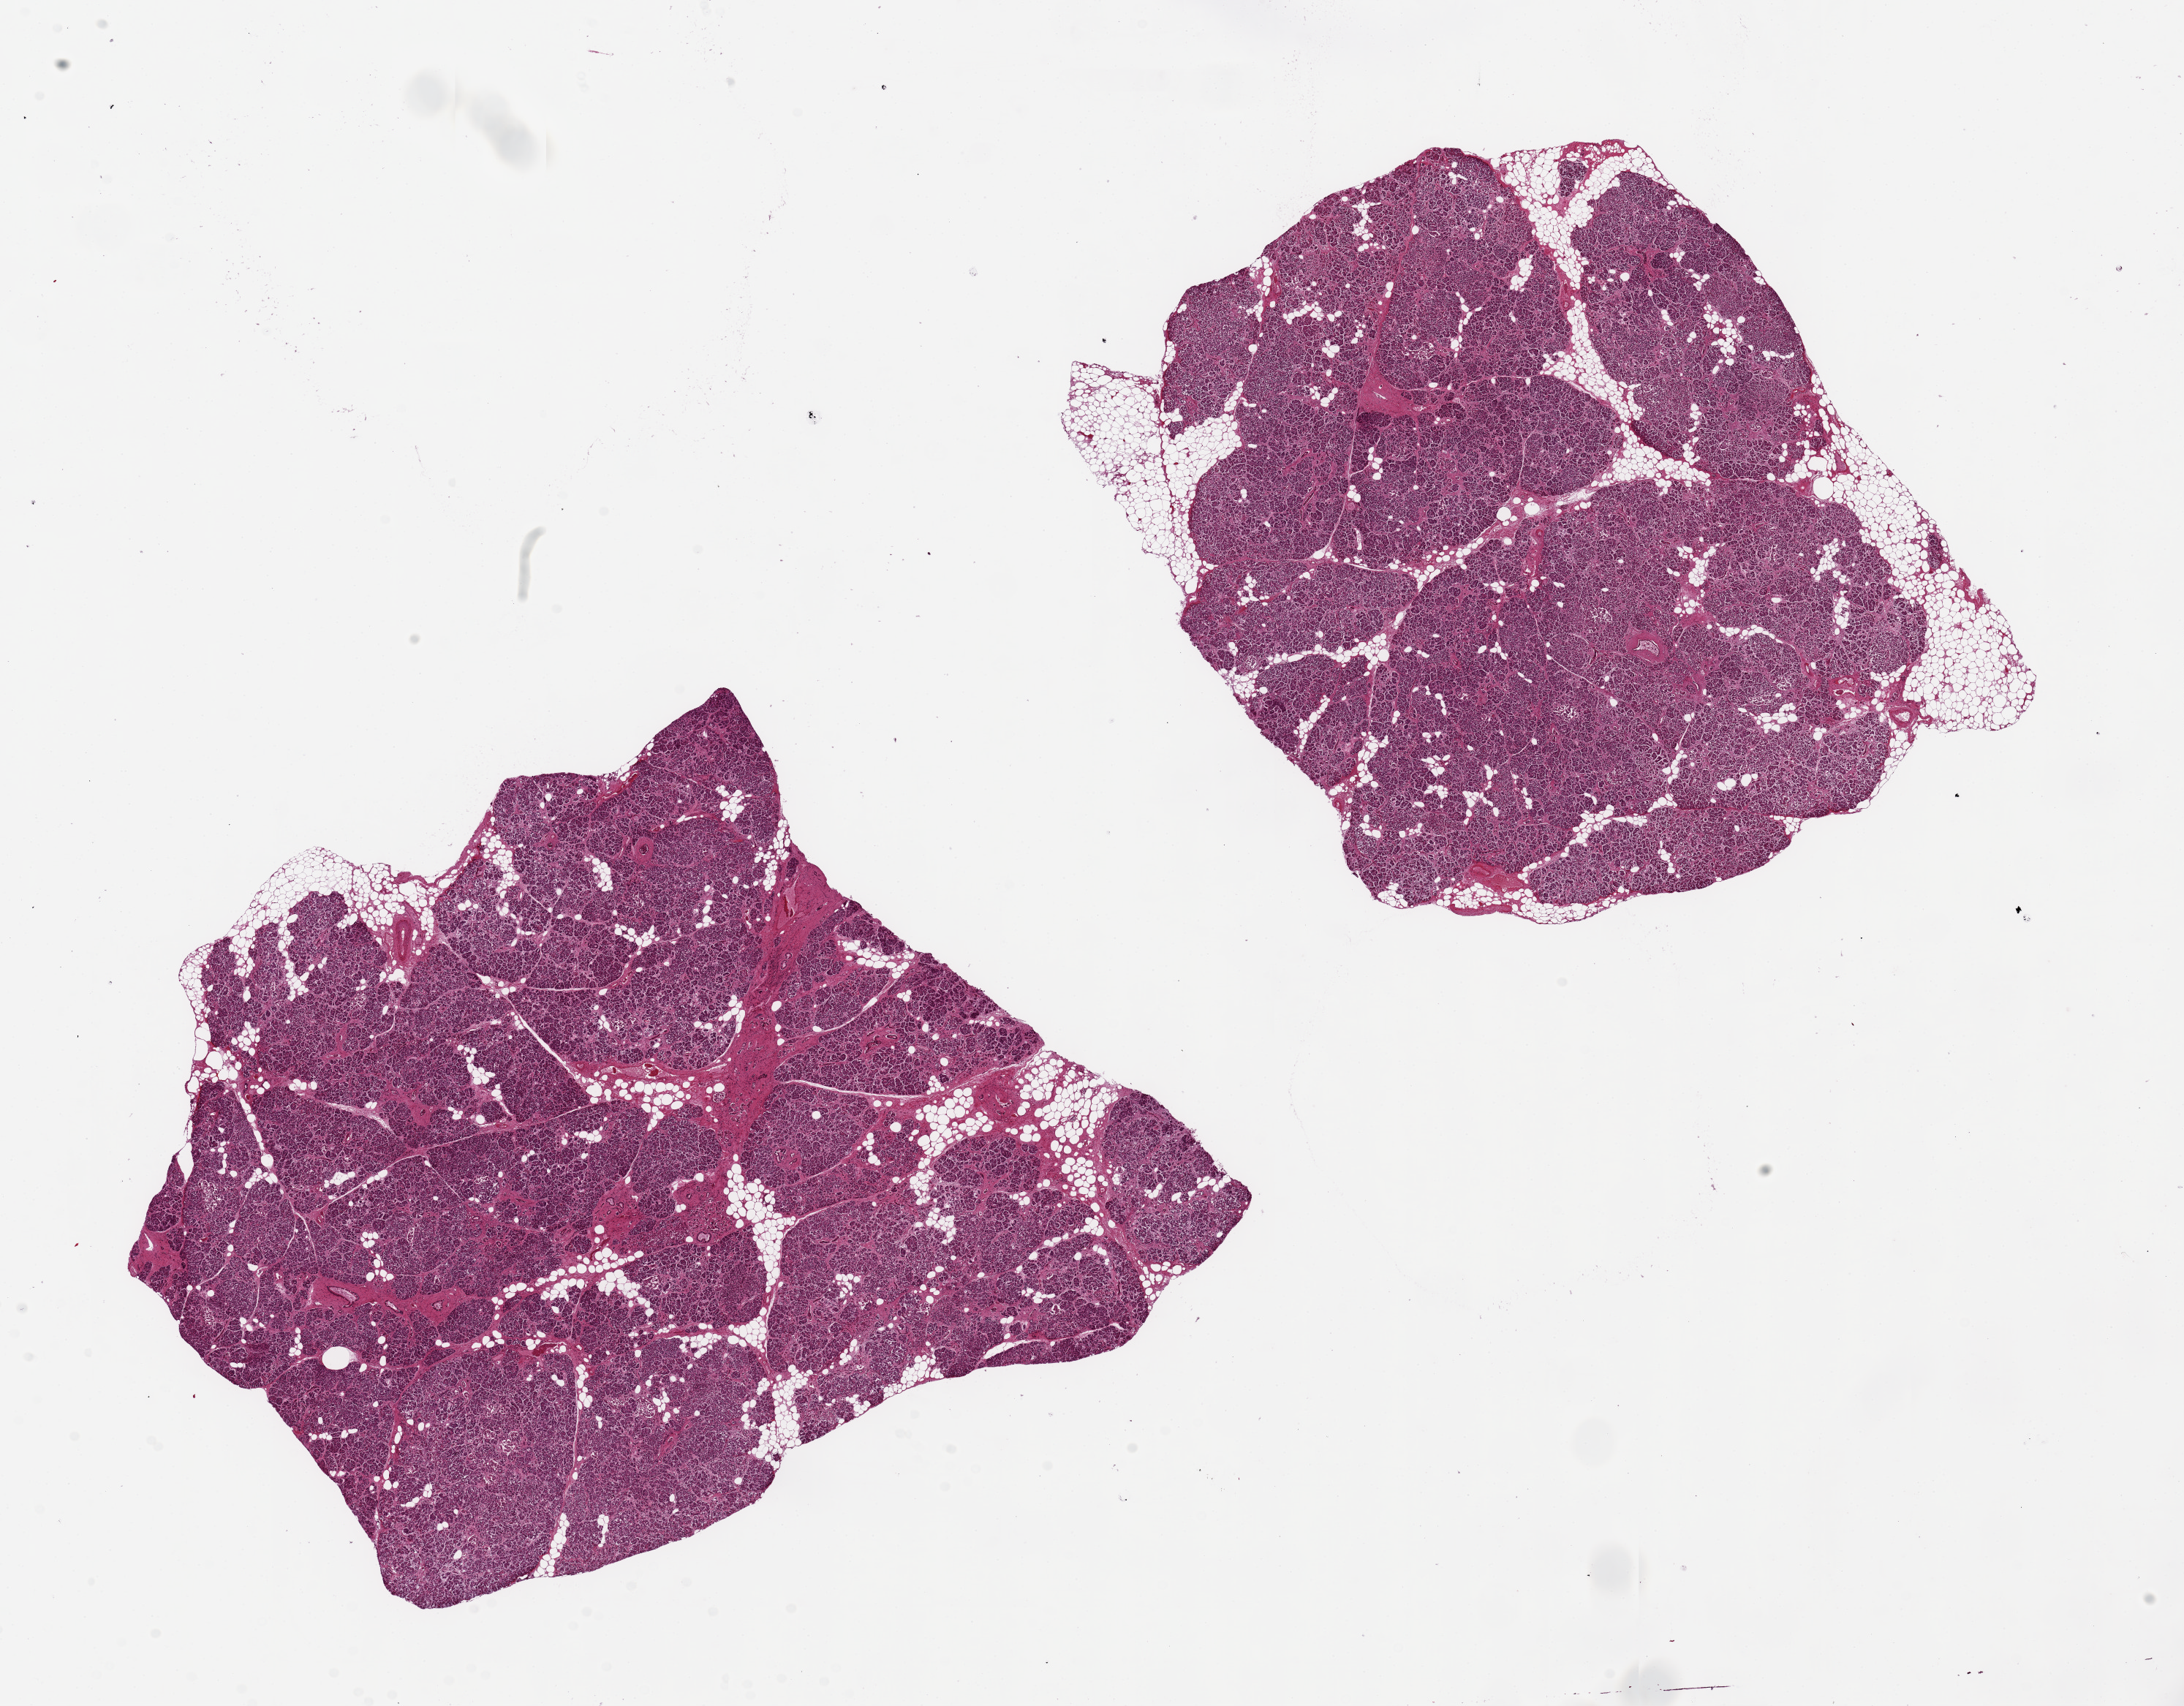
Whole-slide image, haematoxylin and eosin stain — shown as a low-resolution overview of the whole scanned area (about 23.6 x 18.5 mm, slide scanned at 20x), PAXgene-fixed paraffin-embedded (PFPE) section, sampled site (target tissue): pancreas, tissue donor sample. Donor sex: male.
Pathologist's review note for this sample: 2 pieces, 10x9.5 & 8x7.5mm; 10% internal fat.